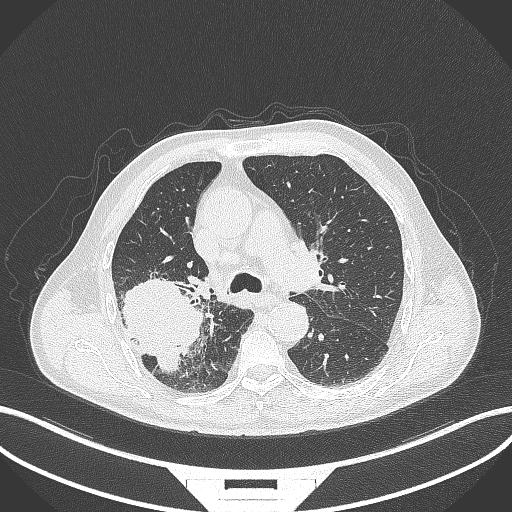
Chest CT, one axial slice; position 265 of 429 along the scan axis; 120 kVp; lung window (W 1500 / L -600 HU); 1 mm slice thickness; 512 × 512 image matrix. Patient: male, 72 years. From the clinical record (not read from this slice): clinical TNM (as recorded): T3 N2 M0.
Structures marked on this image (rectangle marked by the reading radiologist):
- lung tumour (recorded histology: adenocarcinoma): bounding box [x1, y1, x2, y2] px = [113, 270, 209, 375]